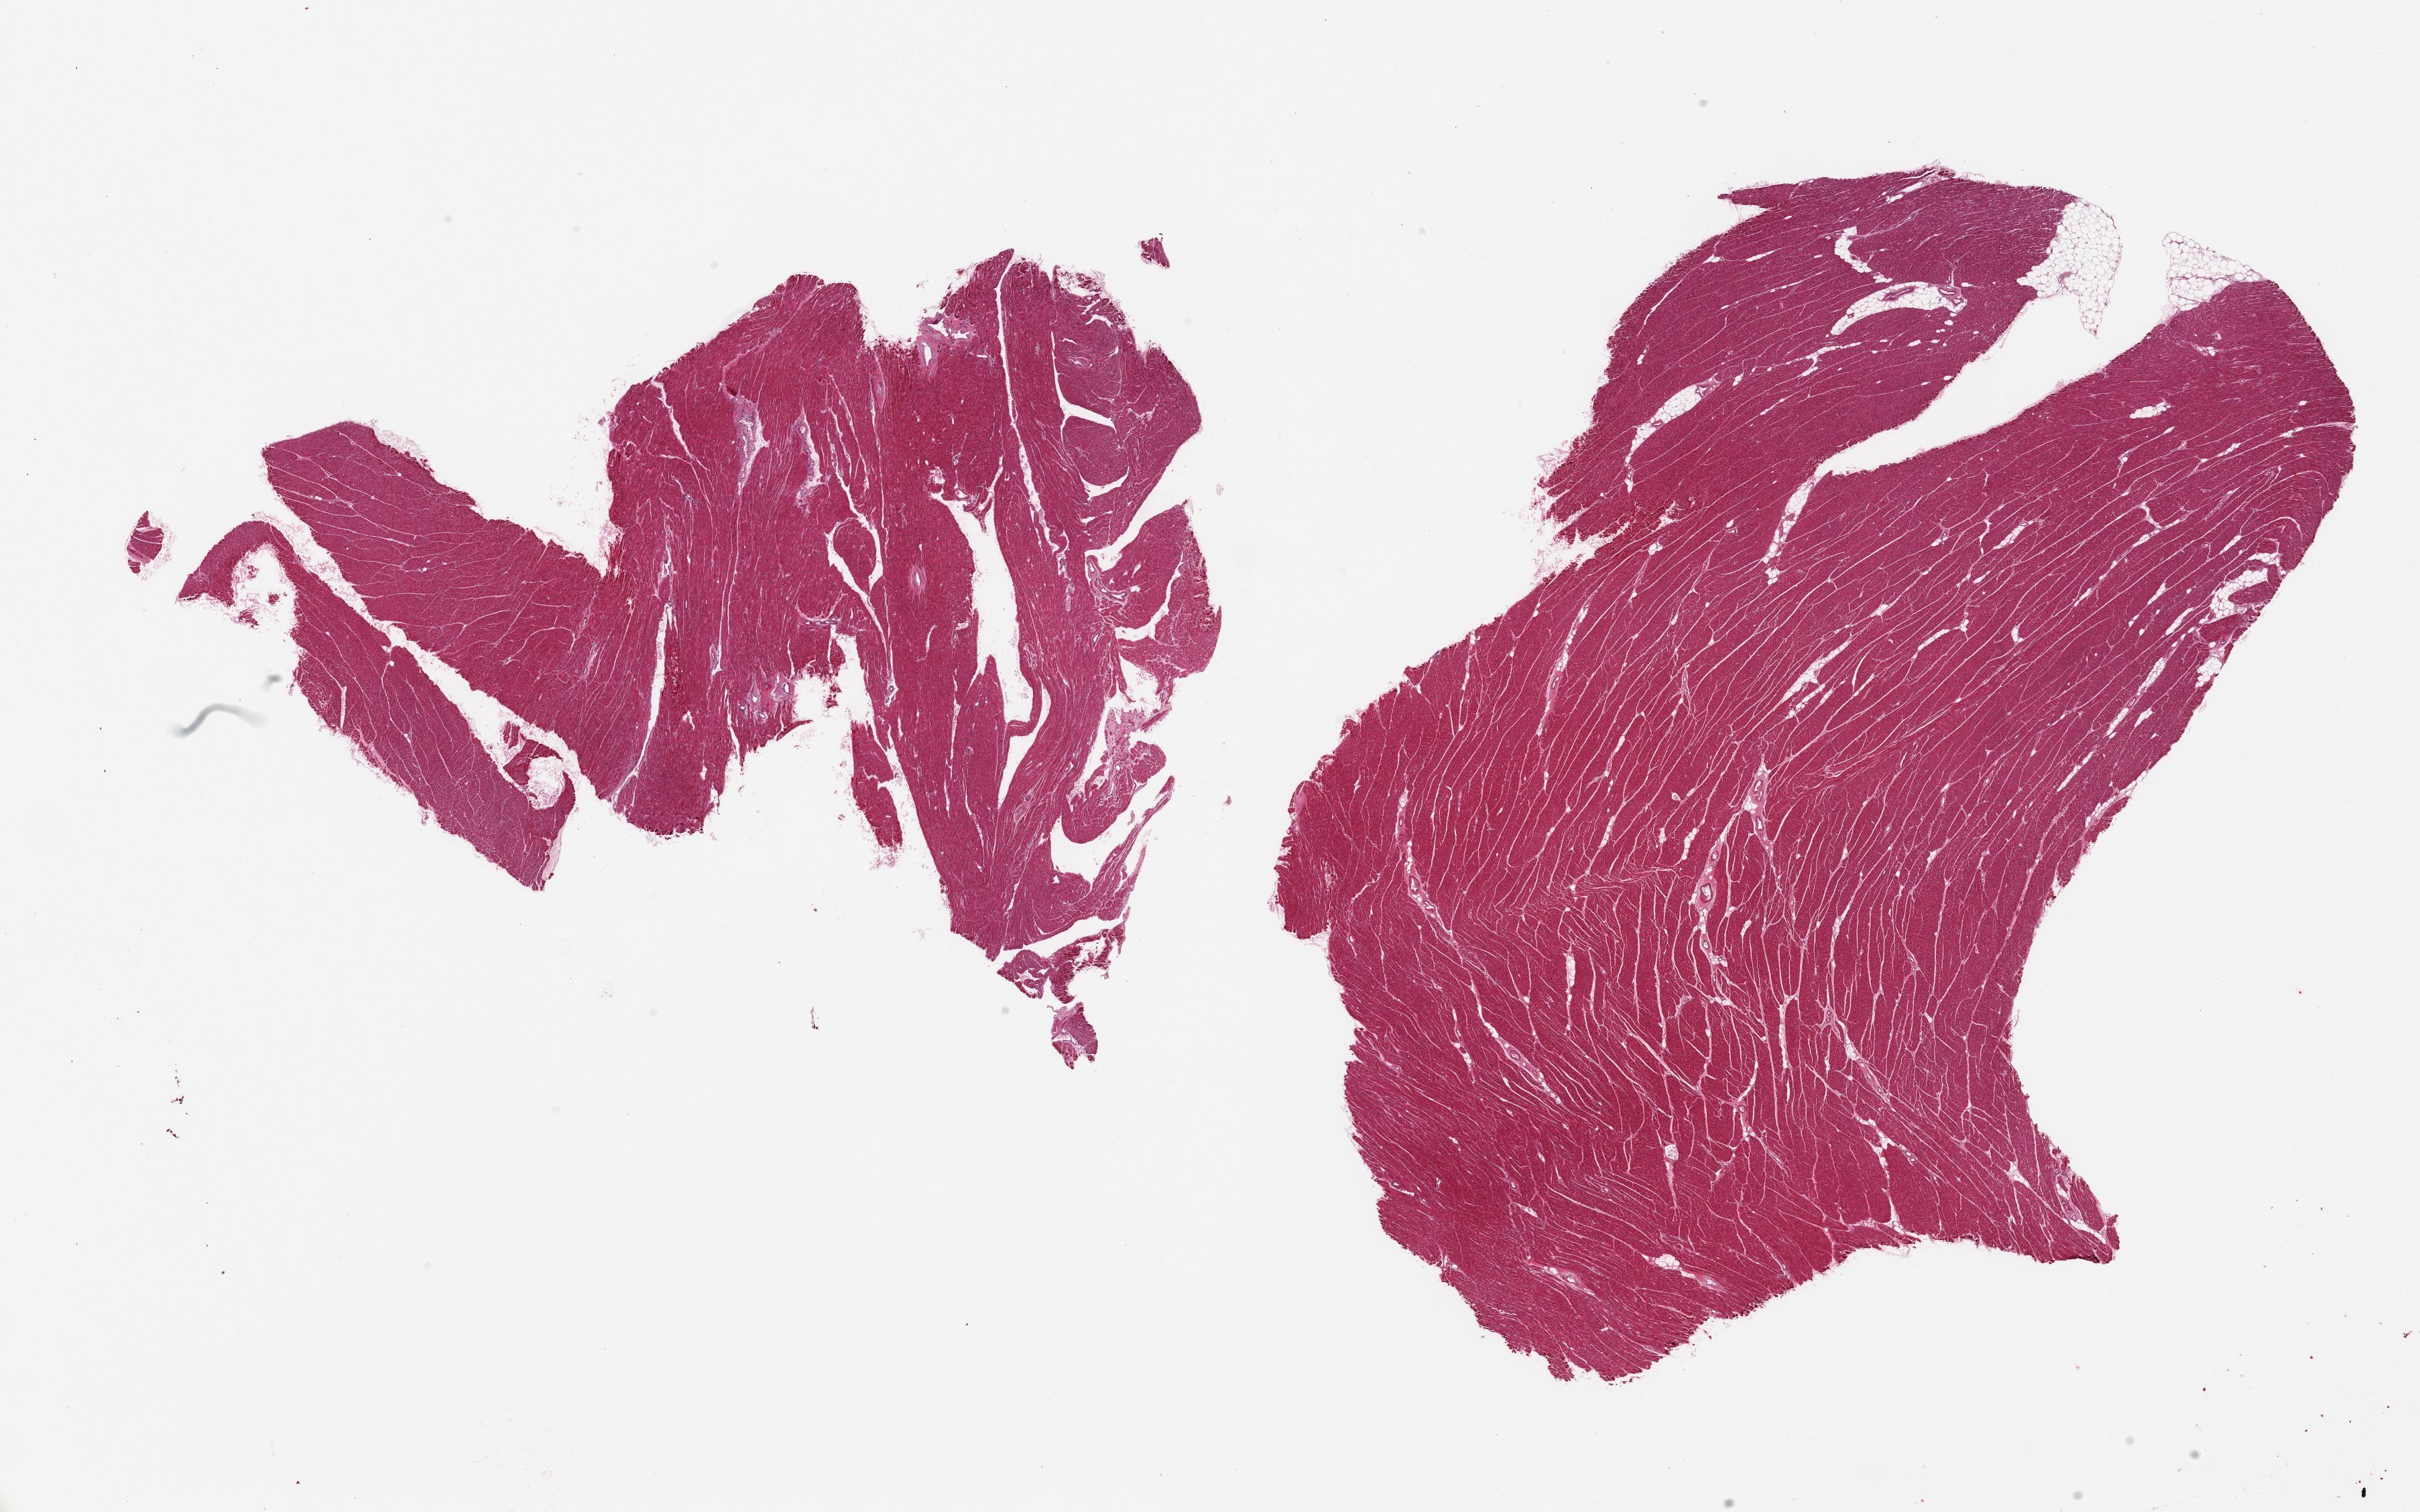
Hematoxylin and eosin (H&E) whole-slide image, shown as a low-resolution overview of the whole scanned area (about 28.5 x 17.8 mm), PAXgene-fixed paraffin-embedded (PFPE) section, section of heart (target tissue), tissue donor sample. Donor sex: female.
• reviewer comment on this tissue sample: 2 pieces, no significant interstitial fibrosis/chronic ischemic changes